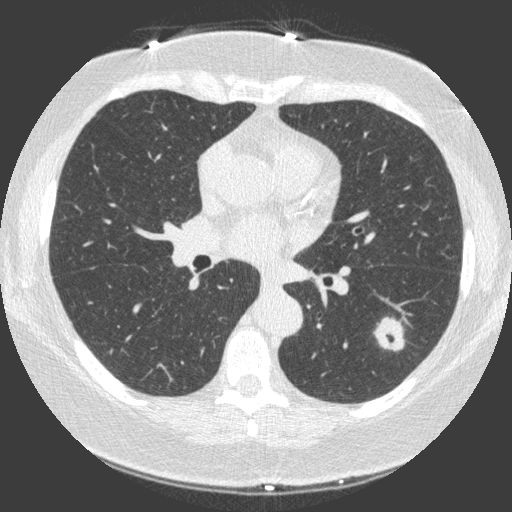
Low-dose screening chest CT, axial slice; third screening round (two years after baseline); lung window (W 1500 / L -600 HU); standard (soft-tissue) reconstruction kernel (C); 512 × 512 image matrix, field of view 330 × 330 mm. Female participant, aged 66 years at enrolment.
Expert reader's lesion annotation, box from (x=363, y=302) to (x=420, y=354) px. Screening reader's record for this exam (one nodule recorded; not confirmed to be the boxed lesion): non-calcified nodule or mass ≥4 mm, left lower lobe, 23 × 17 mm, spiculated (stellate) margins, soft tissue attenuation, pre-existing on the prior screen: yes; interval growth: yes.